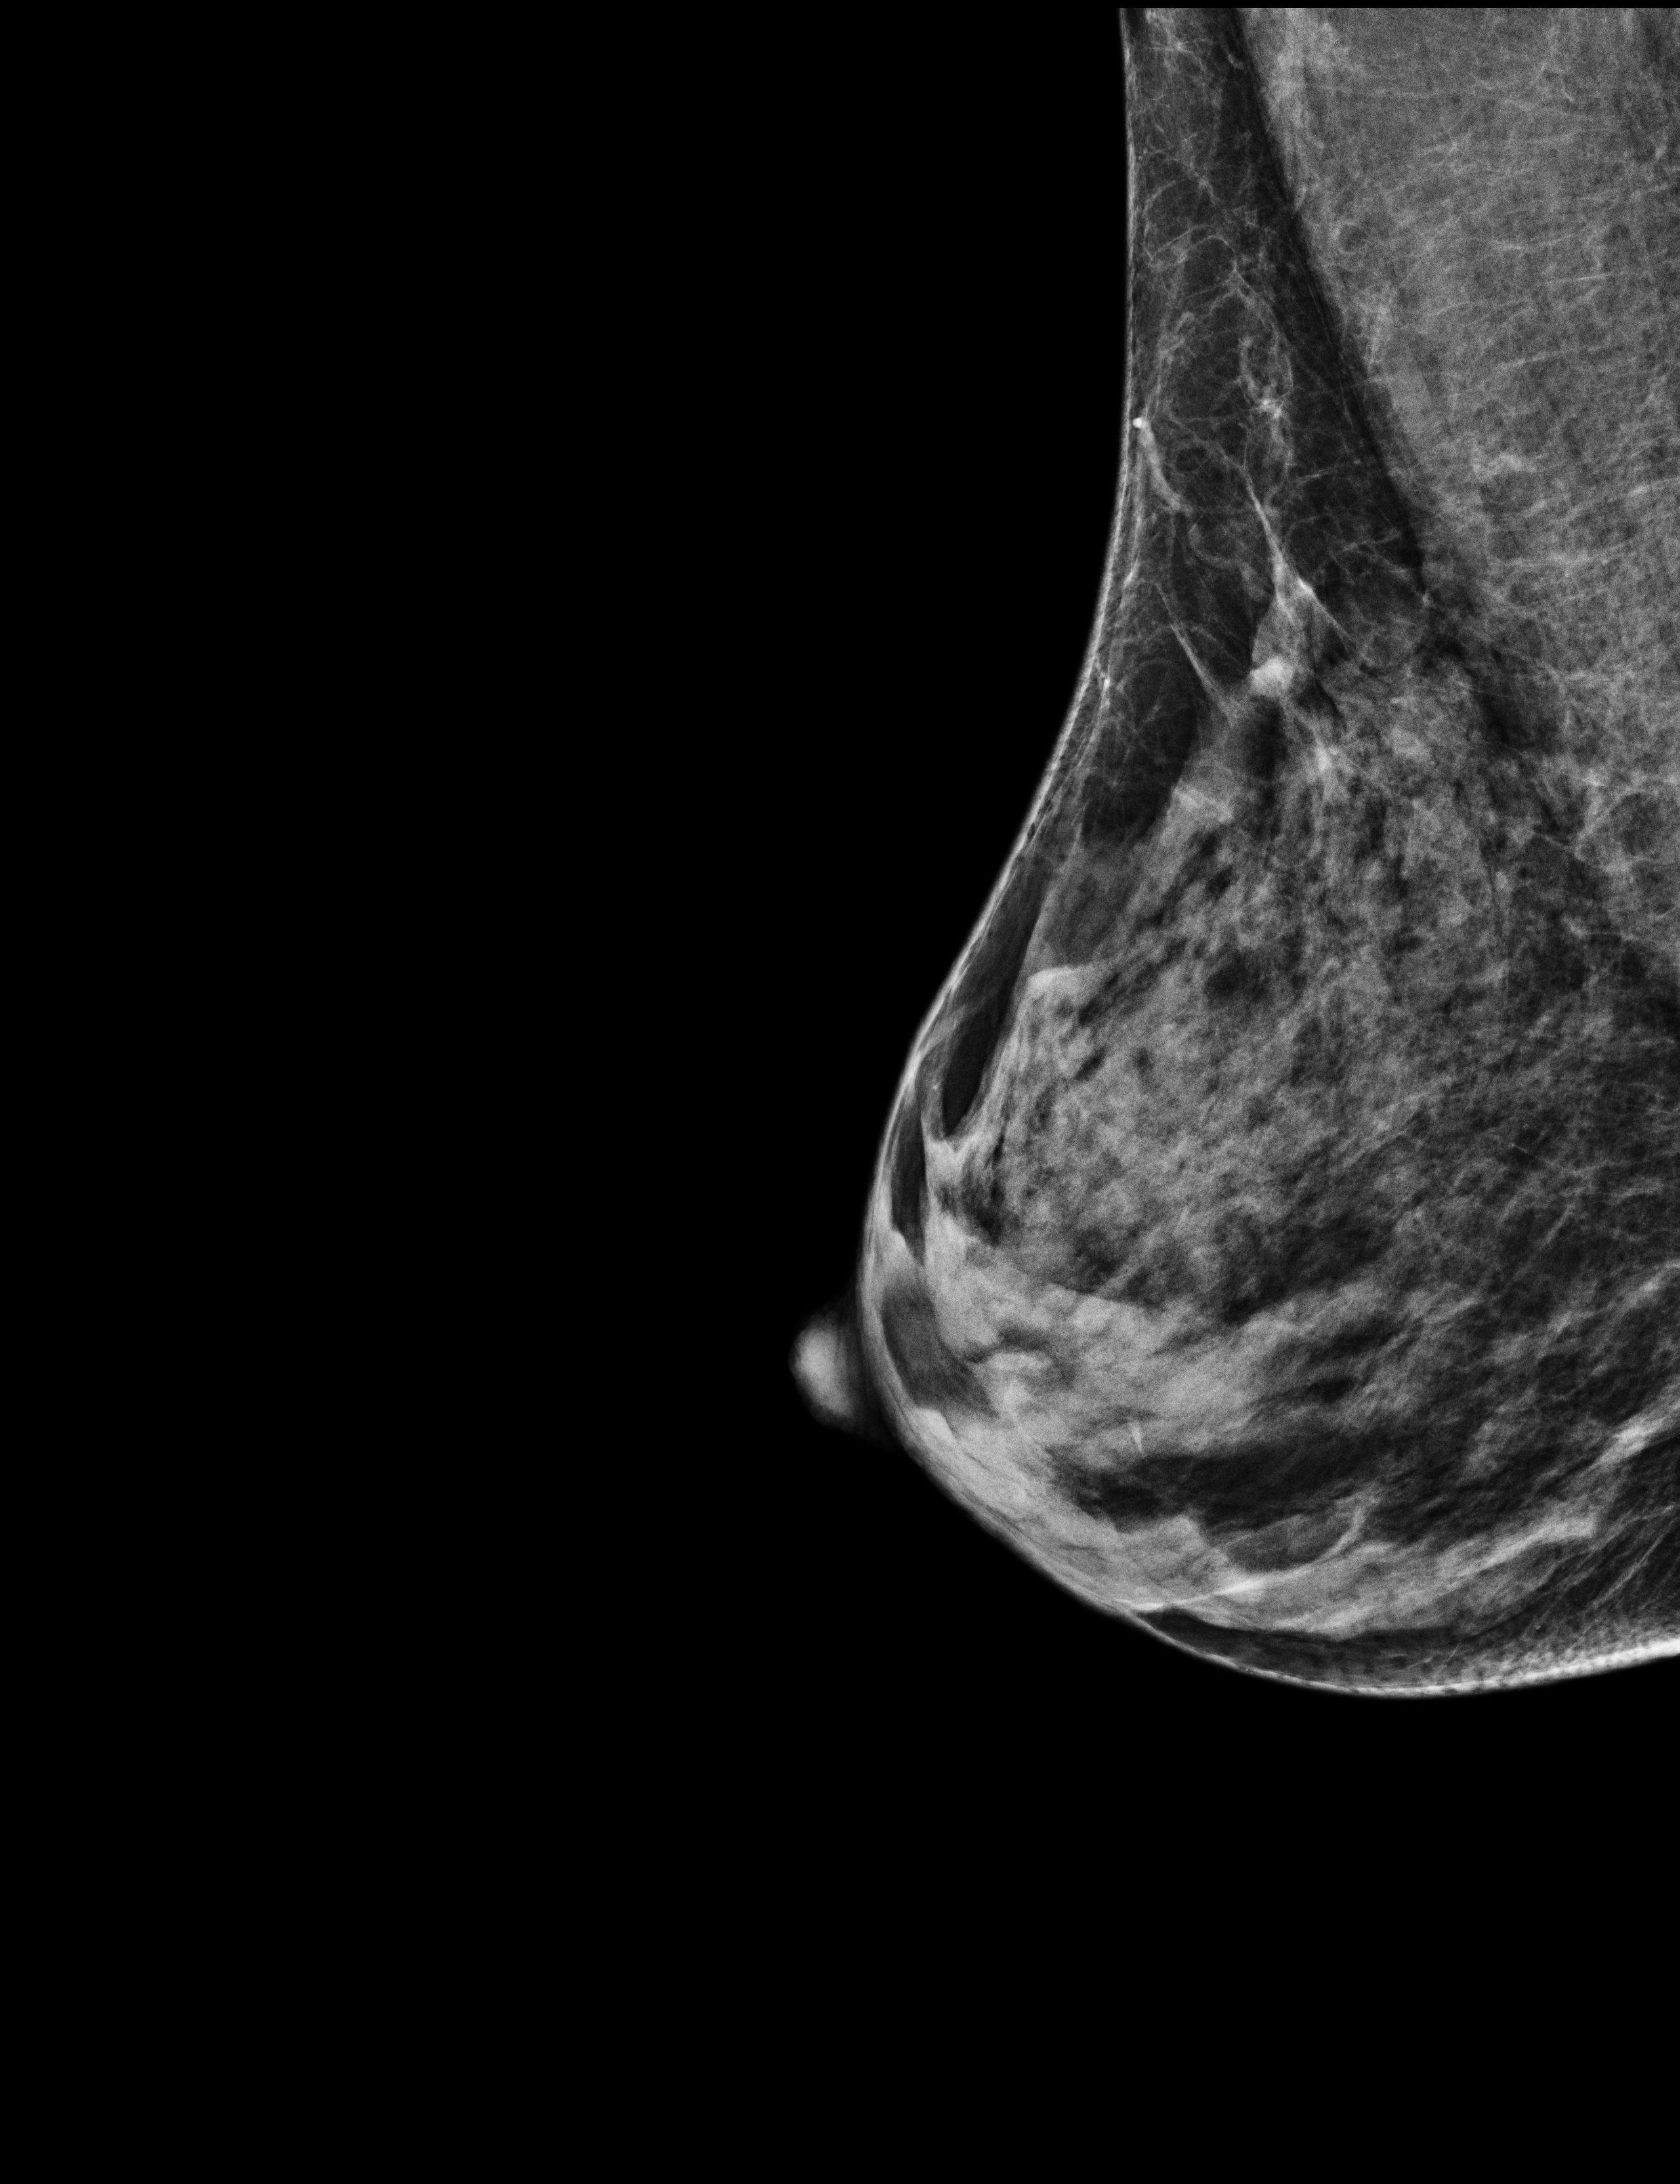
Screening examination; system: Selenia Dimensions. Patient aged 56 years (female).
Image type: full-field digital mammogram. Breast: right. Projection: medio-lateral oblique projection.